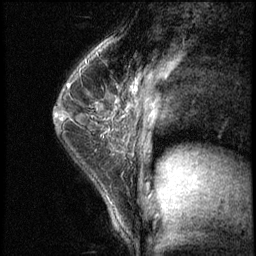
Breast MRI (dynamic contrast-enhanced), one sagittal slice. Slice 41 of 62 in the series (ordered by position). 3 images stored at this slice position (order not interpretable as contrast timing). 1.5 T. TE 4.2 ms, TR 8.7 ms. 2.5 mm slice thickness. 256 × 256 image matrix, field of view 180 × 180 mm. Patient: female, 35 years. Case-level facts recorded for this patient, not image findings: setting: breast cancer imaged before/during neoadjuvant chemotherapy; receptor status: HER2-positive.
Annotated regions visible in this slice (semi-automatic segmentation, software-assisted and operator-edited):
- analysis volume of interest (the breast-tissue region the enhancement analysis was run in; not a lesion): bounding box (x1, y1, x2, y2) in pixels: (71, 78, 120, 139)
- tumour enhancement mask (voxels above the 140 % enhancement threshold inside the analysis volume of interest): (106, 117, 113, 120)